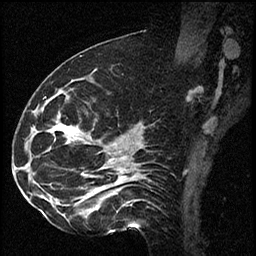
Breast MRI (dynamic contrast-enhanced), one sagittal slice. Dynamic contrast-enhanced series, image 2 of 2 at this slice position (ordered by acquisition). 1.5 T. TE 4.2 ms, TR 17.3 ms. 256 × 256 image matrix, field of view 200 × 200 mm. Female patient. From the clinical record (not read from this slice): setting: breast cancer imaged before/during neoadjuvant chemotherapy; receptor status: HR-positive, HER2-negative.
Outlined on this slice (semi-automatic segmentation, software-assisted and operator-edited):
- analysis volume of interest (the breast-tissue region the enhancement analysis was run in; not a lesion): bounding box [x1, y1, x2, y2] px = [41, 93, 115, 223]
- tumour enhancement mask (voxels above the 100 % enhancement threshold inside the analysis volume of interest): [56, 126, 77, 132]